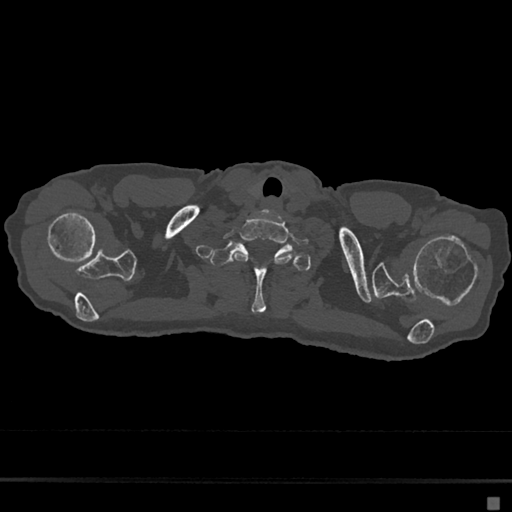
CT including the spine, one axial slice; slice 626 of 797 in the series (ordered by position); bone window (W 1800 / L 400 HU); 0.5 mm slice thickness; 512 × 512 image matrix, field of view 360 × 360 mm. Patient: female, 68 years. From the clinical record (not read from this slice): primary cancer: renal.
Annotated regions visible in this slice (semi-automatically segmented with operator editing):
- T1 vertebra: bounding box [x1, y1, x2, y2] px = [209, 242, 312, 314]